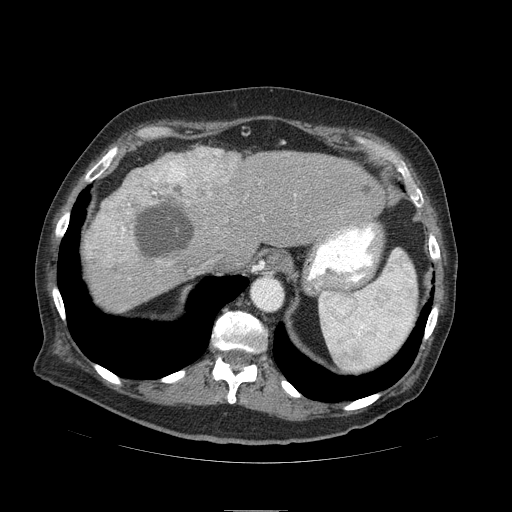
Contrast-enhanced abdominal CT (liver protocol), one axial slice. Position 73 of 103 along the scan axis. 120 kVp. Soft-tissue window (W 400 / L 40 HU). 2.5 mm slice thickness. 512 × 512 image matrix. Case-level facts recorded for this patient, not image findings: diagnosis: hepatocellular carcinoma (patient treated with transarterial chemoembolisation; whether this scan precedes or follows treatment is not stated here); TNM stage (as recorded): Stage-IIIA; Child-Pugh class: B.
Outlined on this slice (semi-automatic segmentation, software-assisted and operator-edited):
- abdominal aorta: bounding box [x1, y1, x2, y2] px = [252, 277, 282, 310]
- liver parenchyma outside the tumour (the mass and vessels are separate outlines, so this box may not span the whole liver): [83, 146, 384, 310]
- mass: [89, 150, 244, 262]